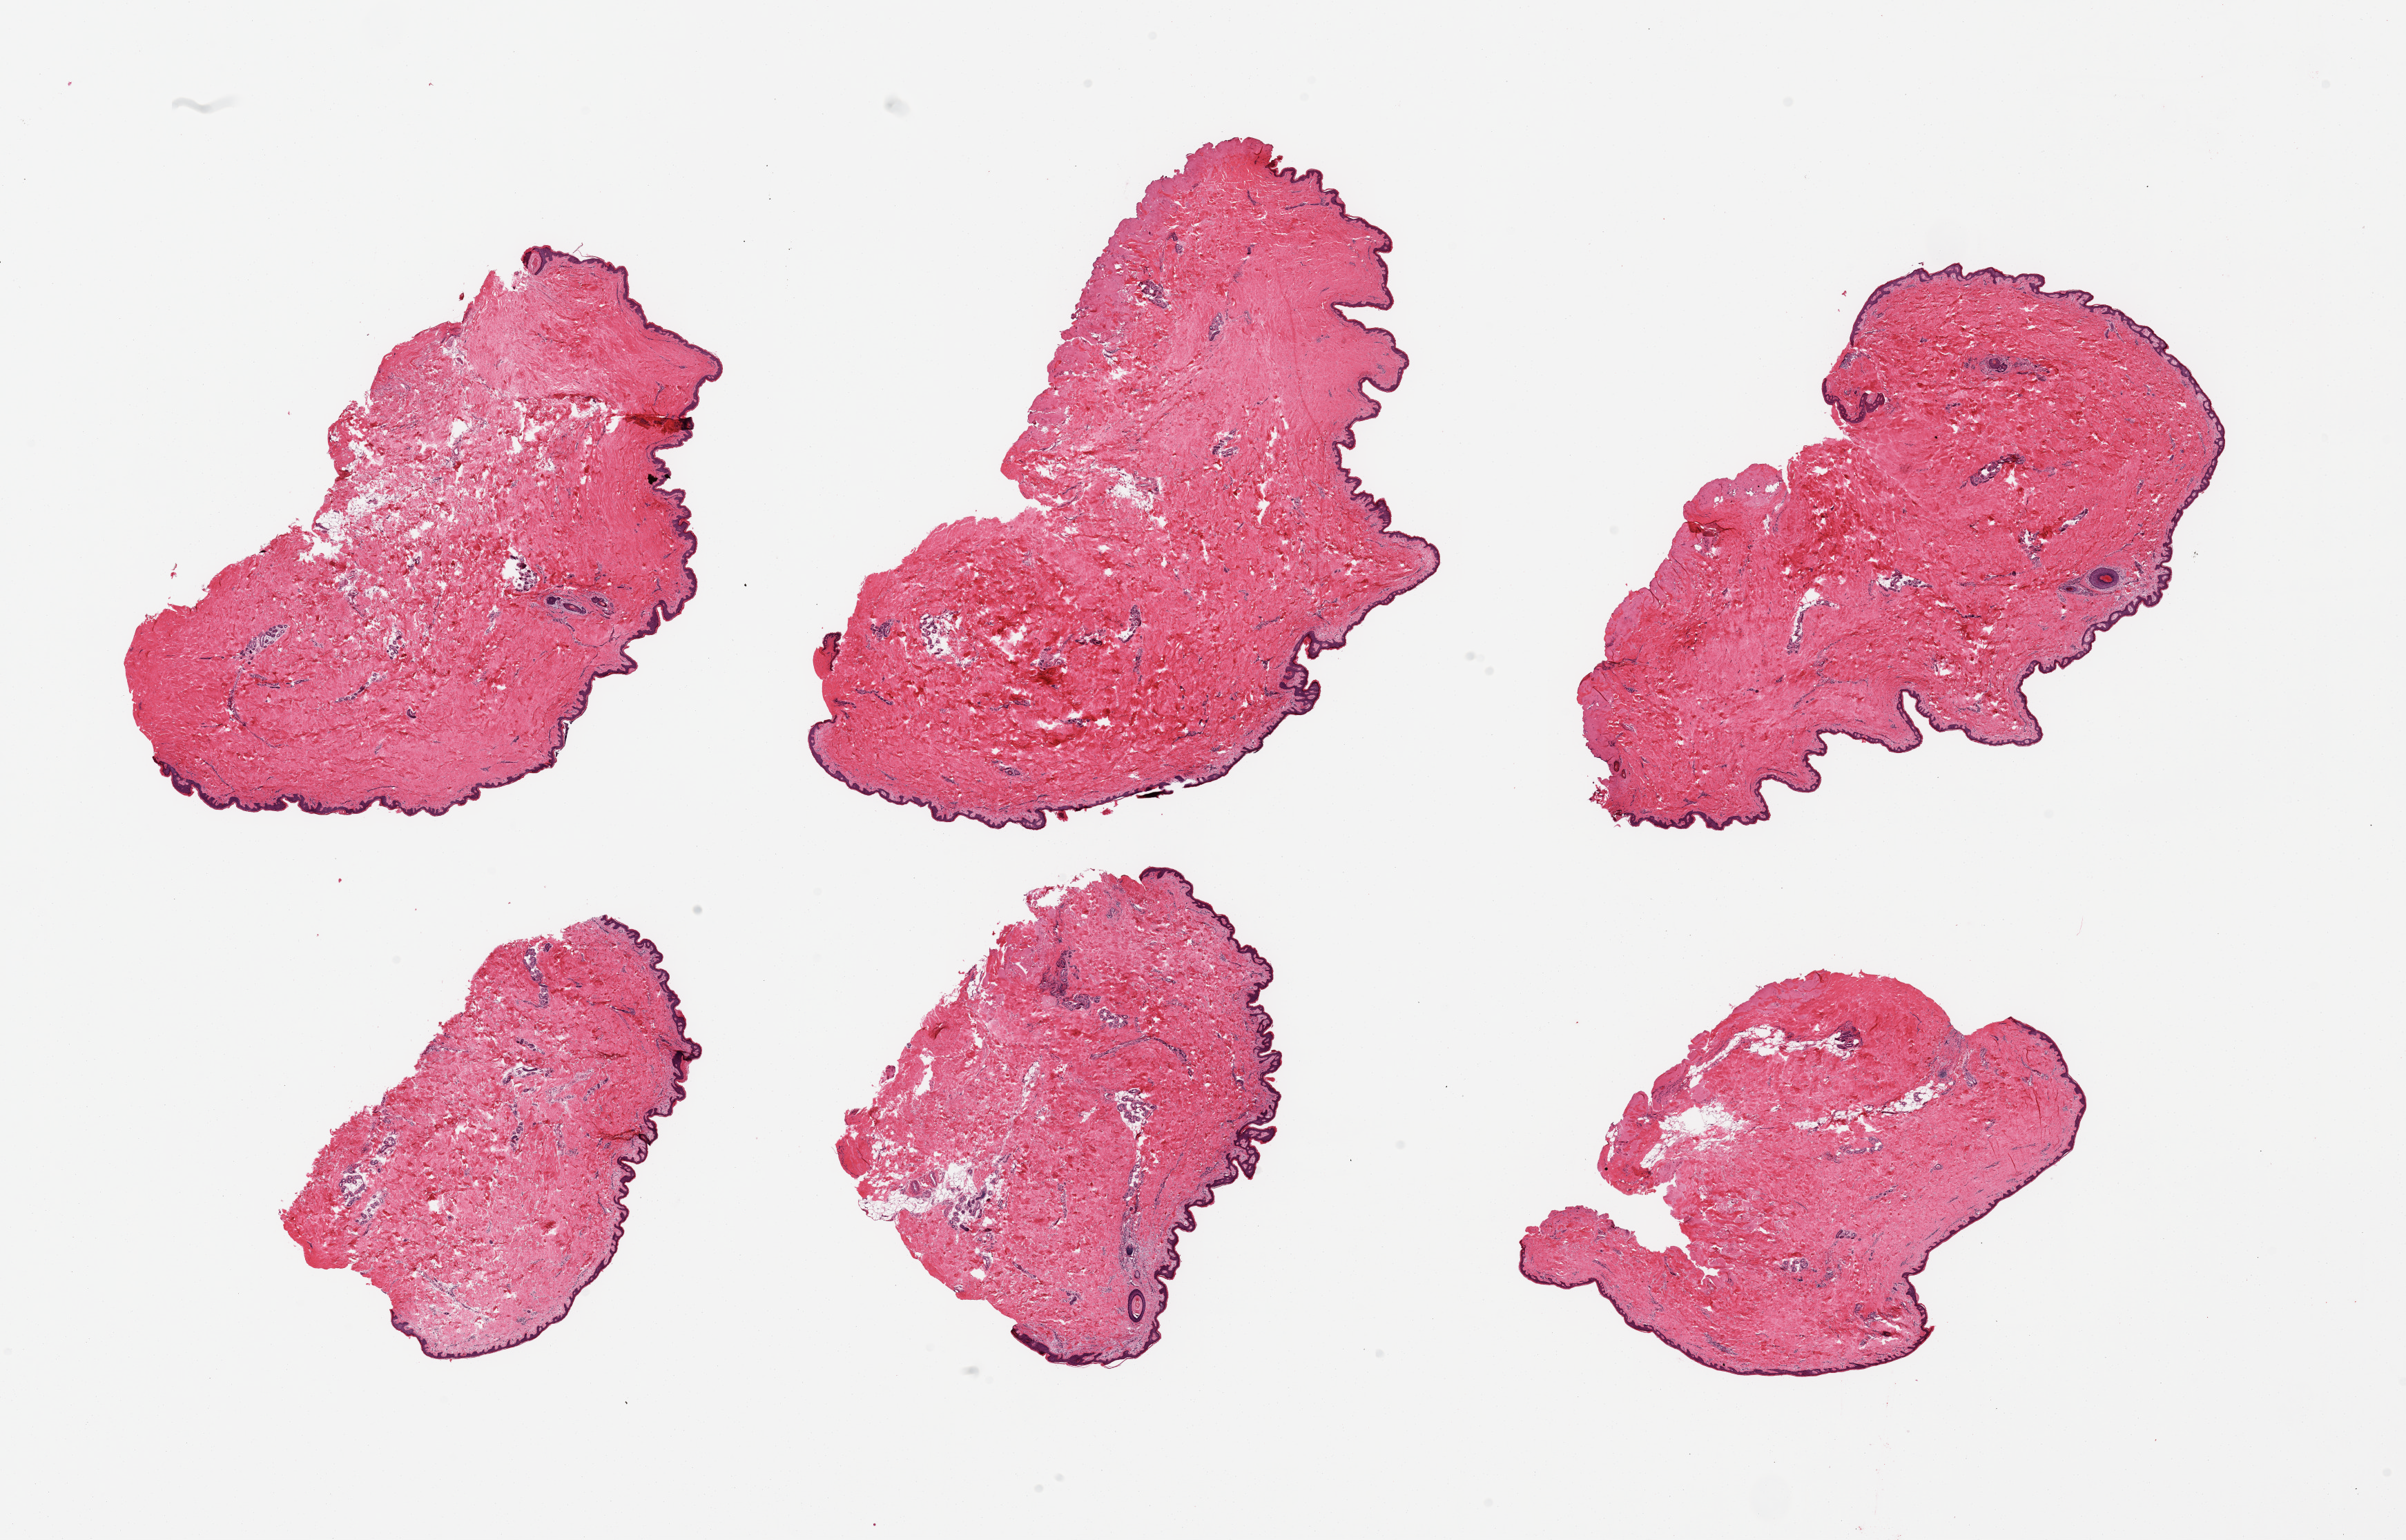
Hematoxylin and eosin (H&E) whole-slide image, whole scanned area (about 27.6 x 17.6 mm, acquisition: 20x scan) shown as a low-resolution overview, PAXgene-fixed paraffin-embedded (PFPE) section, target tissue: skin of suprapubic region, donor tissue sample. Donor: female.
Pathologist's review note for this sample: 6 pieces, no dermal fat, squamous epithelium is ~35 microns.